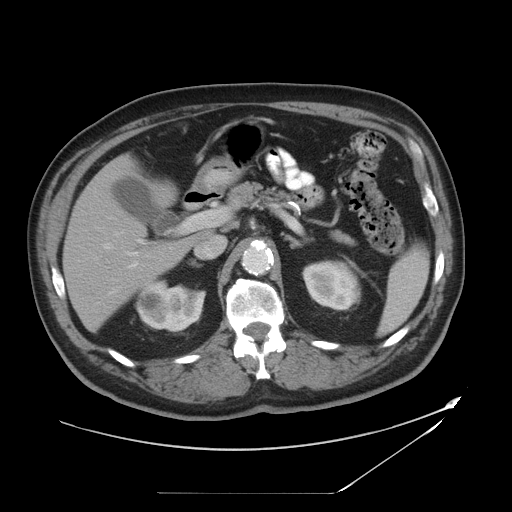
Contrast-enhanced abdominal CT, one axial slice. Slice 25 of 49 in the series (ordered by position). Reconstruction kernel STANDARD. 120 kVp. Intravenous contrast given. Soft-tissue window (W 400 / L 40 HU). 5 mm slice thickness. 512 × 512 image matrix, field of view 461 × 461 mm. Male patient, age 72 years. Case-level facts recorded for this patient, not image findings: diagnosis: colorectal cancer liver metastases, imaged before liver resection; multiple liver metastases: no; largest metastasis: 2.5 cm; disease in both lobes: no.
Structures marked on this image (outlined manually by an expert reader):
- hepatic veins: bounding box <102,231,124,250> (left, top, right, bottom; pixels)
- liver: <64,160,195,329>
- planned liver remnant (the part of the liver to remain after resection): <64,161,185,329>
- portal vein (with intrahepatic branches): <127,210,216,268>